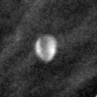
Cropped region of a digitized screen-film mammogram centred on a radiologist-marked abnormality, right breast, MLO view.
Finding: calcifications, morphology lucent center; BI-RADS assessment category 2; benign without callback (not worked up further).